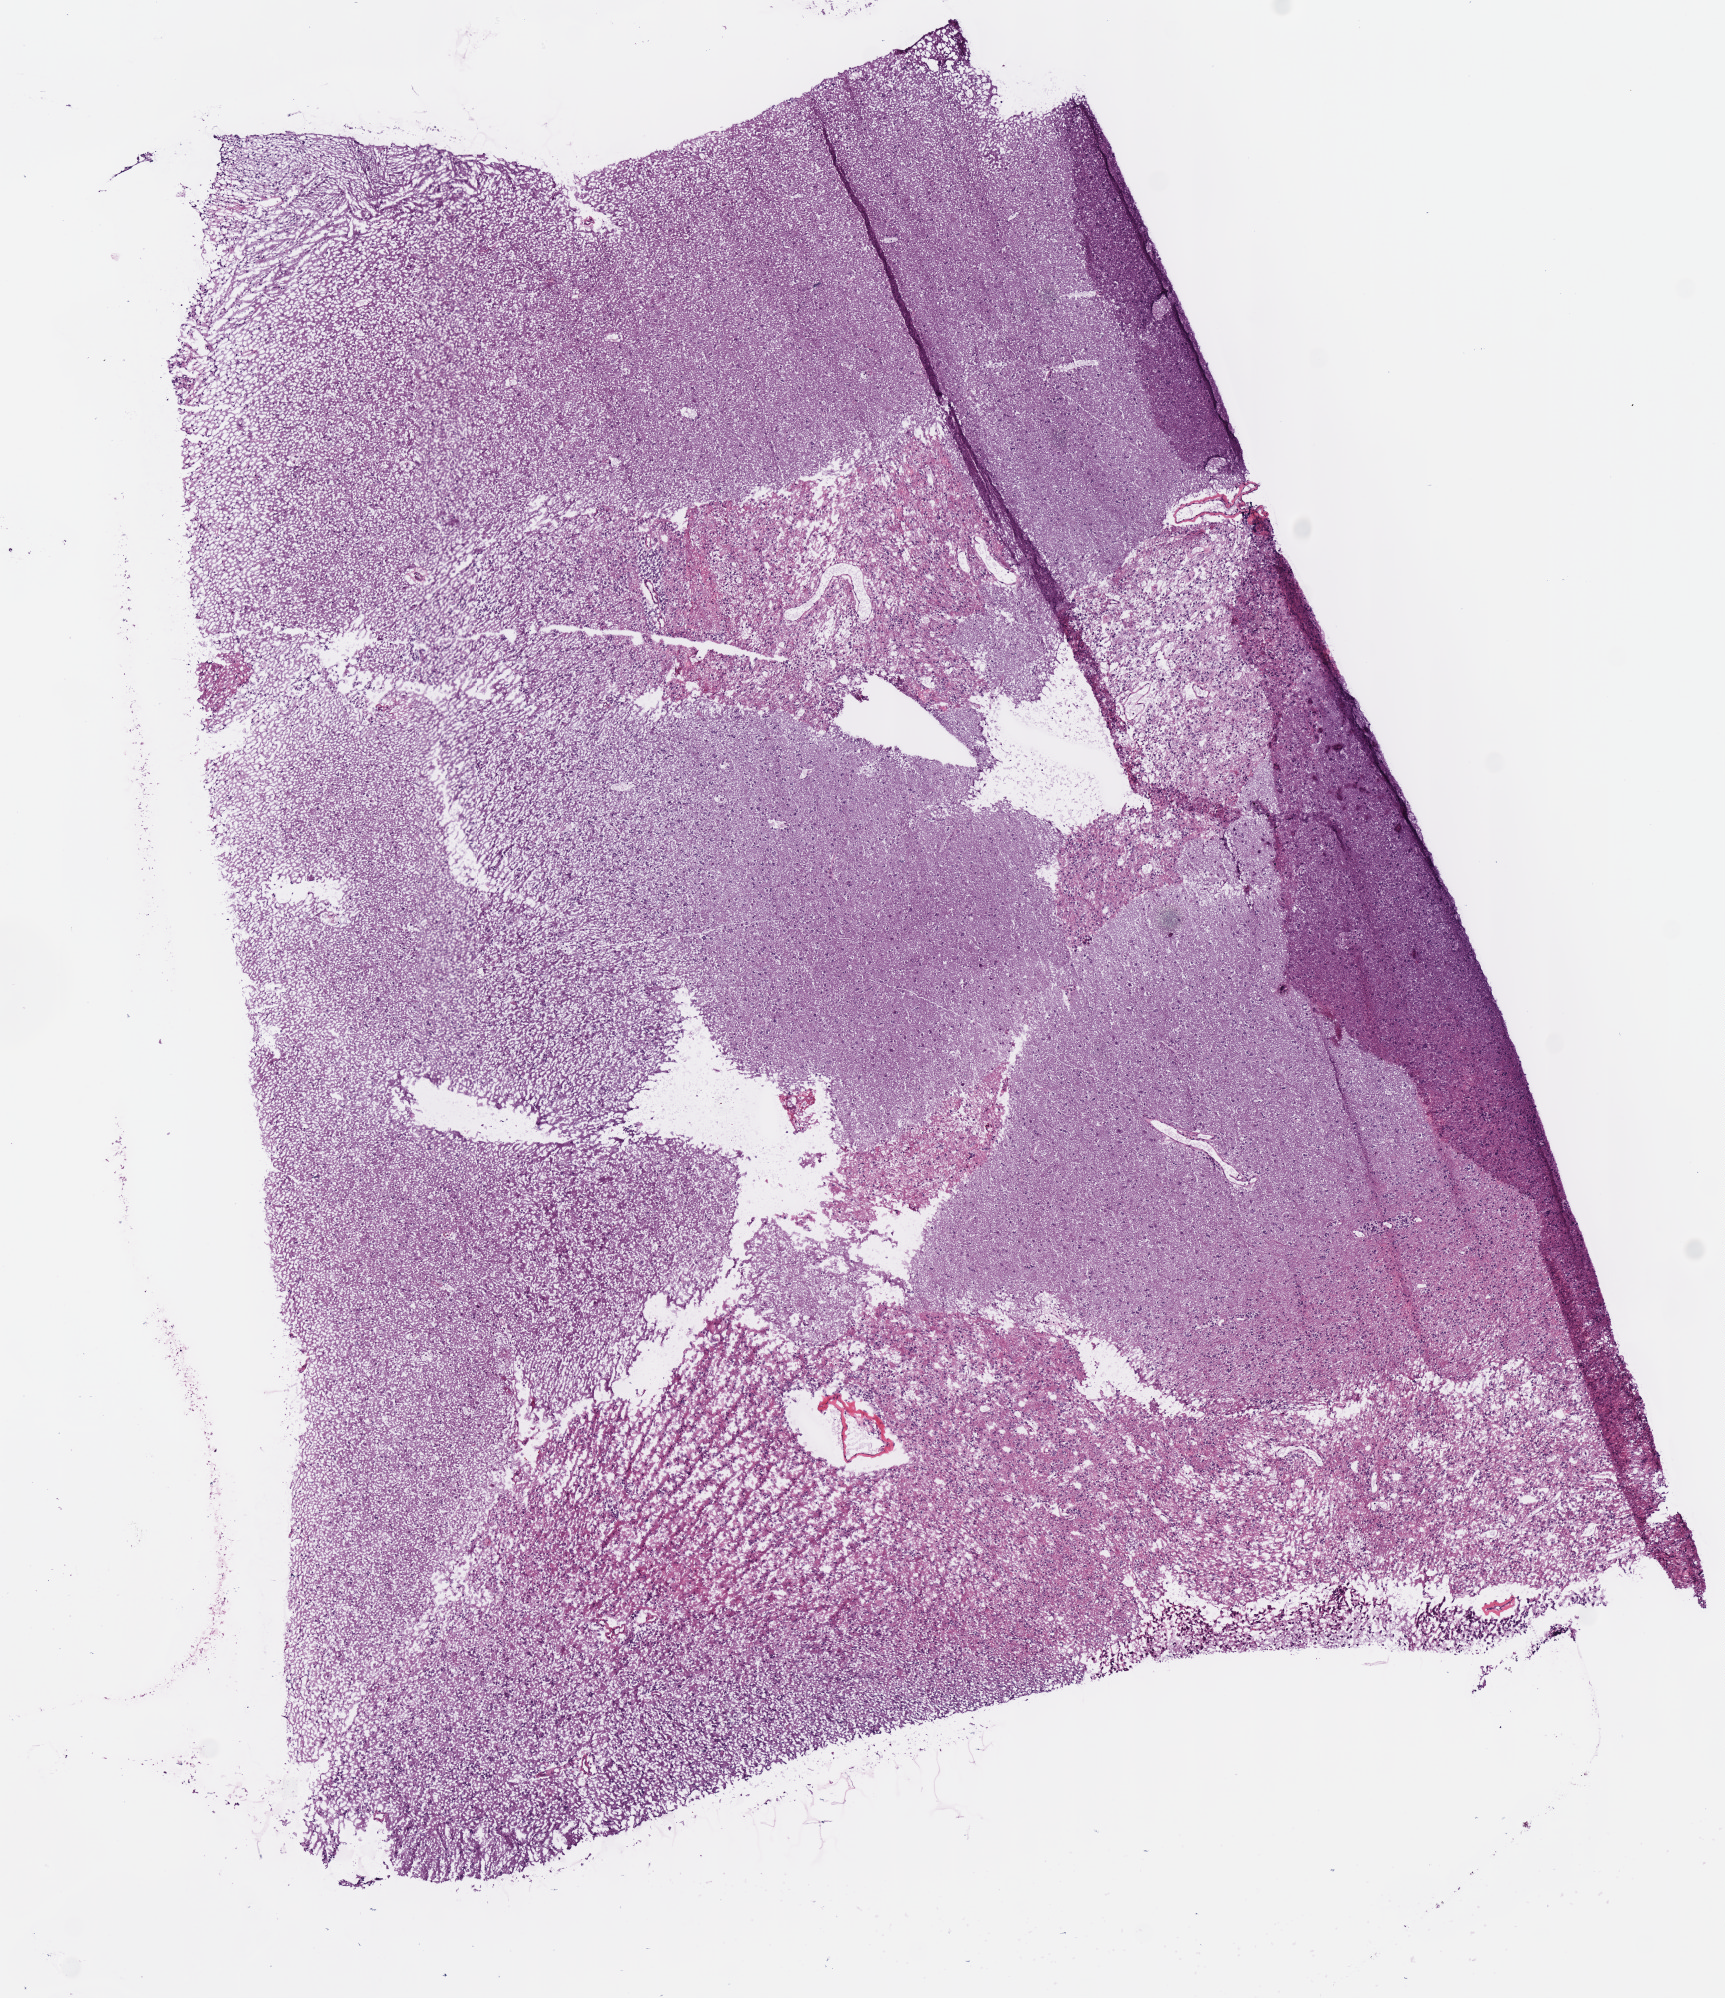
Whole-slide histology image, Hematoxylin and eosin (H&E) stained, low-resolution overview of the scanned area, about 6.8 x 7.9 mm (acquisition: 40x scan); frozen section from the bottom of the tissue portion; sample: primary tumour, brain. Male patient; age at initial diagnosis 39 years. Histologic grade: G2 (moderately differentiated). Composition of this section per pathologist review: tumour cells 70%, tumour nuclei 30%, normal cells 30%, stromal cells 0%, necrosis 0%.
Diagnosis: Oligodendroglioma, NOS (cerebrum).